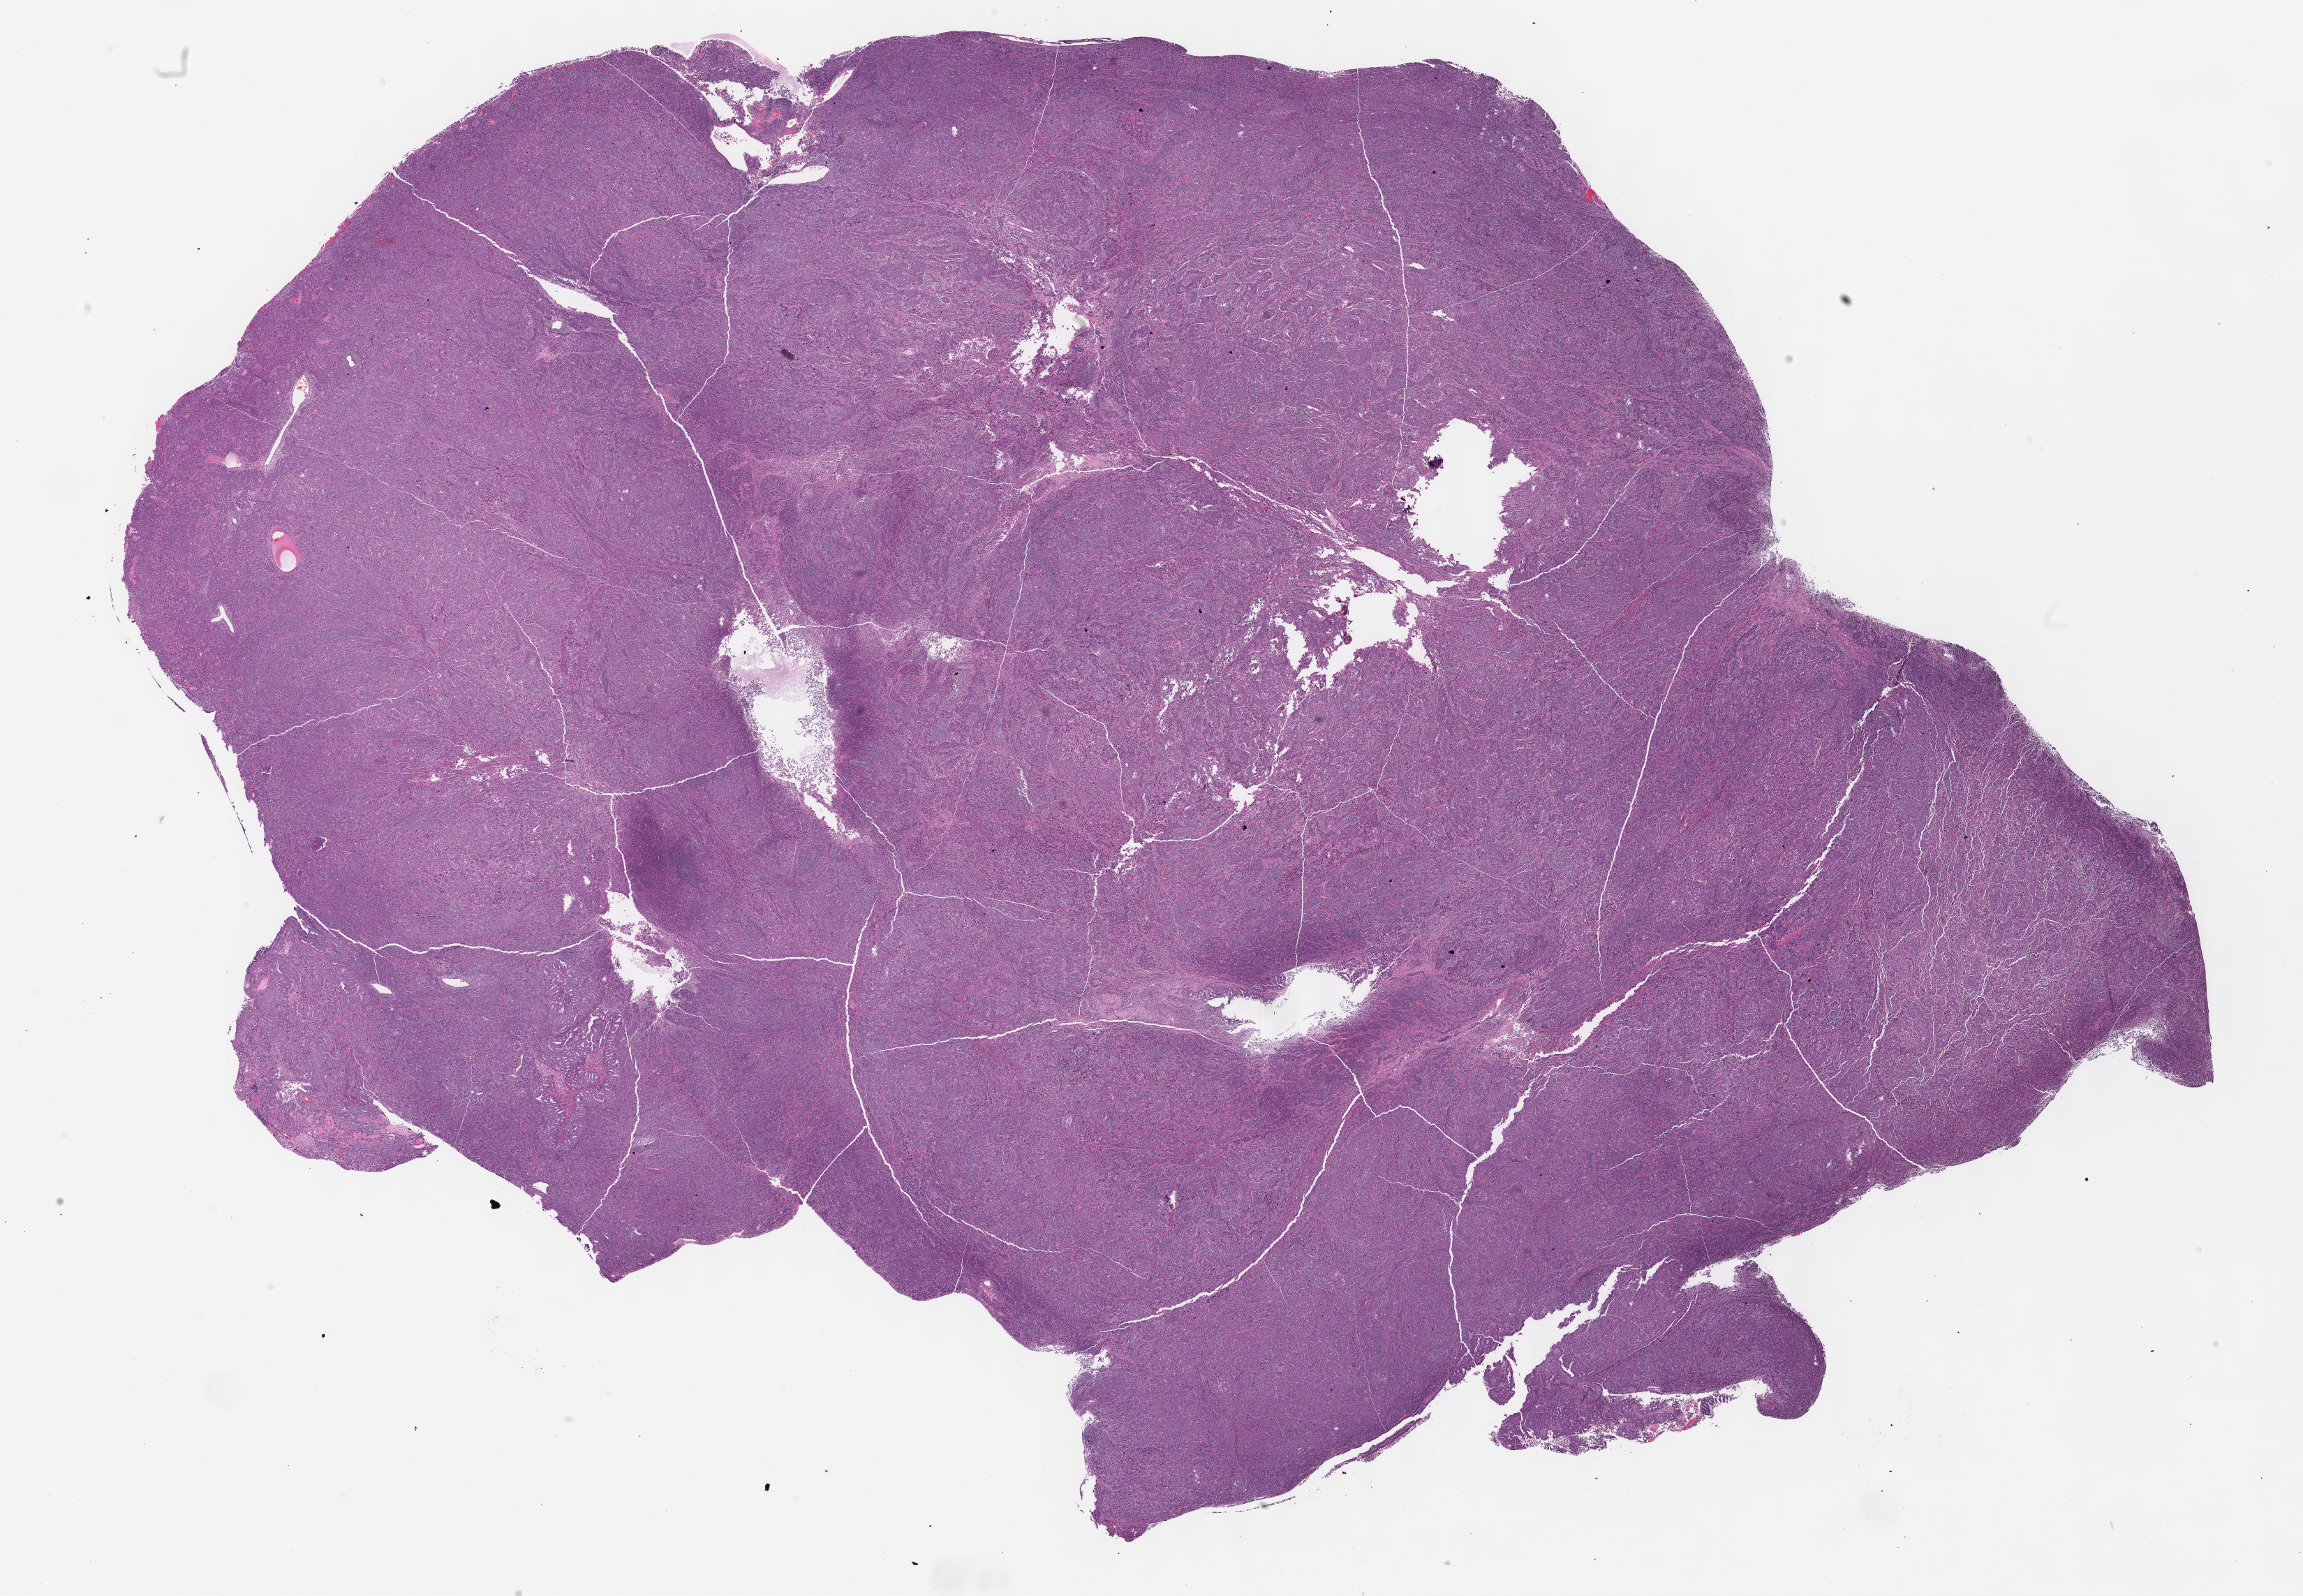
Whole-slide histology image, Hematoxylin and eosin (H&E) stained, low-resolution overview of the scanned area, about 26.7 x 18.5 mm, formalin-fixed paraffin-embedded (FFPE) diagnostic section, sample: primary tumour, uterus. Female, age 59 years at initial diagnosis. Histologic grade: G2 (moderately differentiated).
- histologic diagnosis: Endometrioid adenocarcinoma, NOS (fundus uteri)
- FIGO stage: III